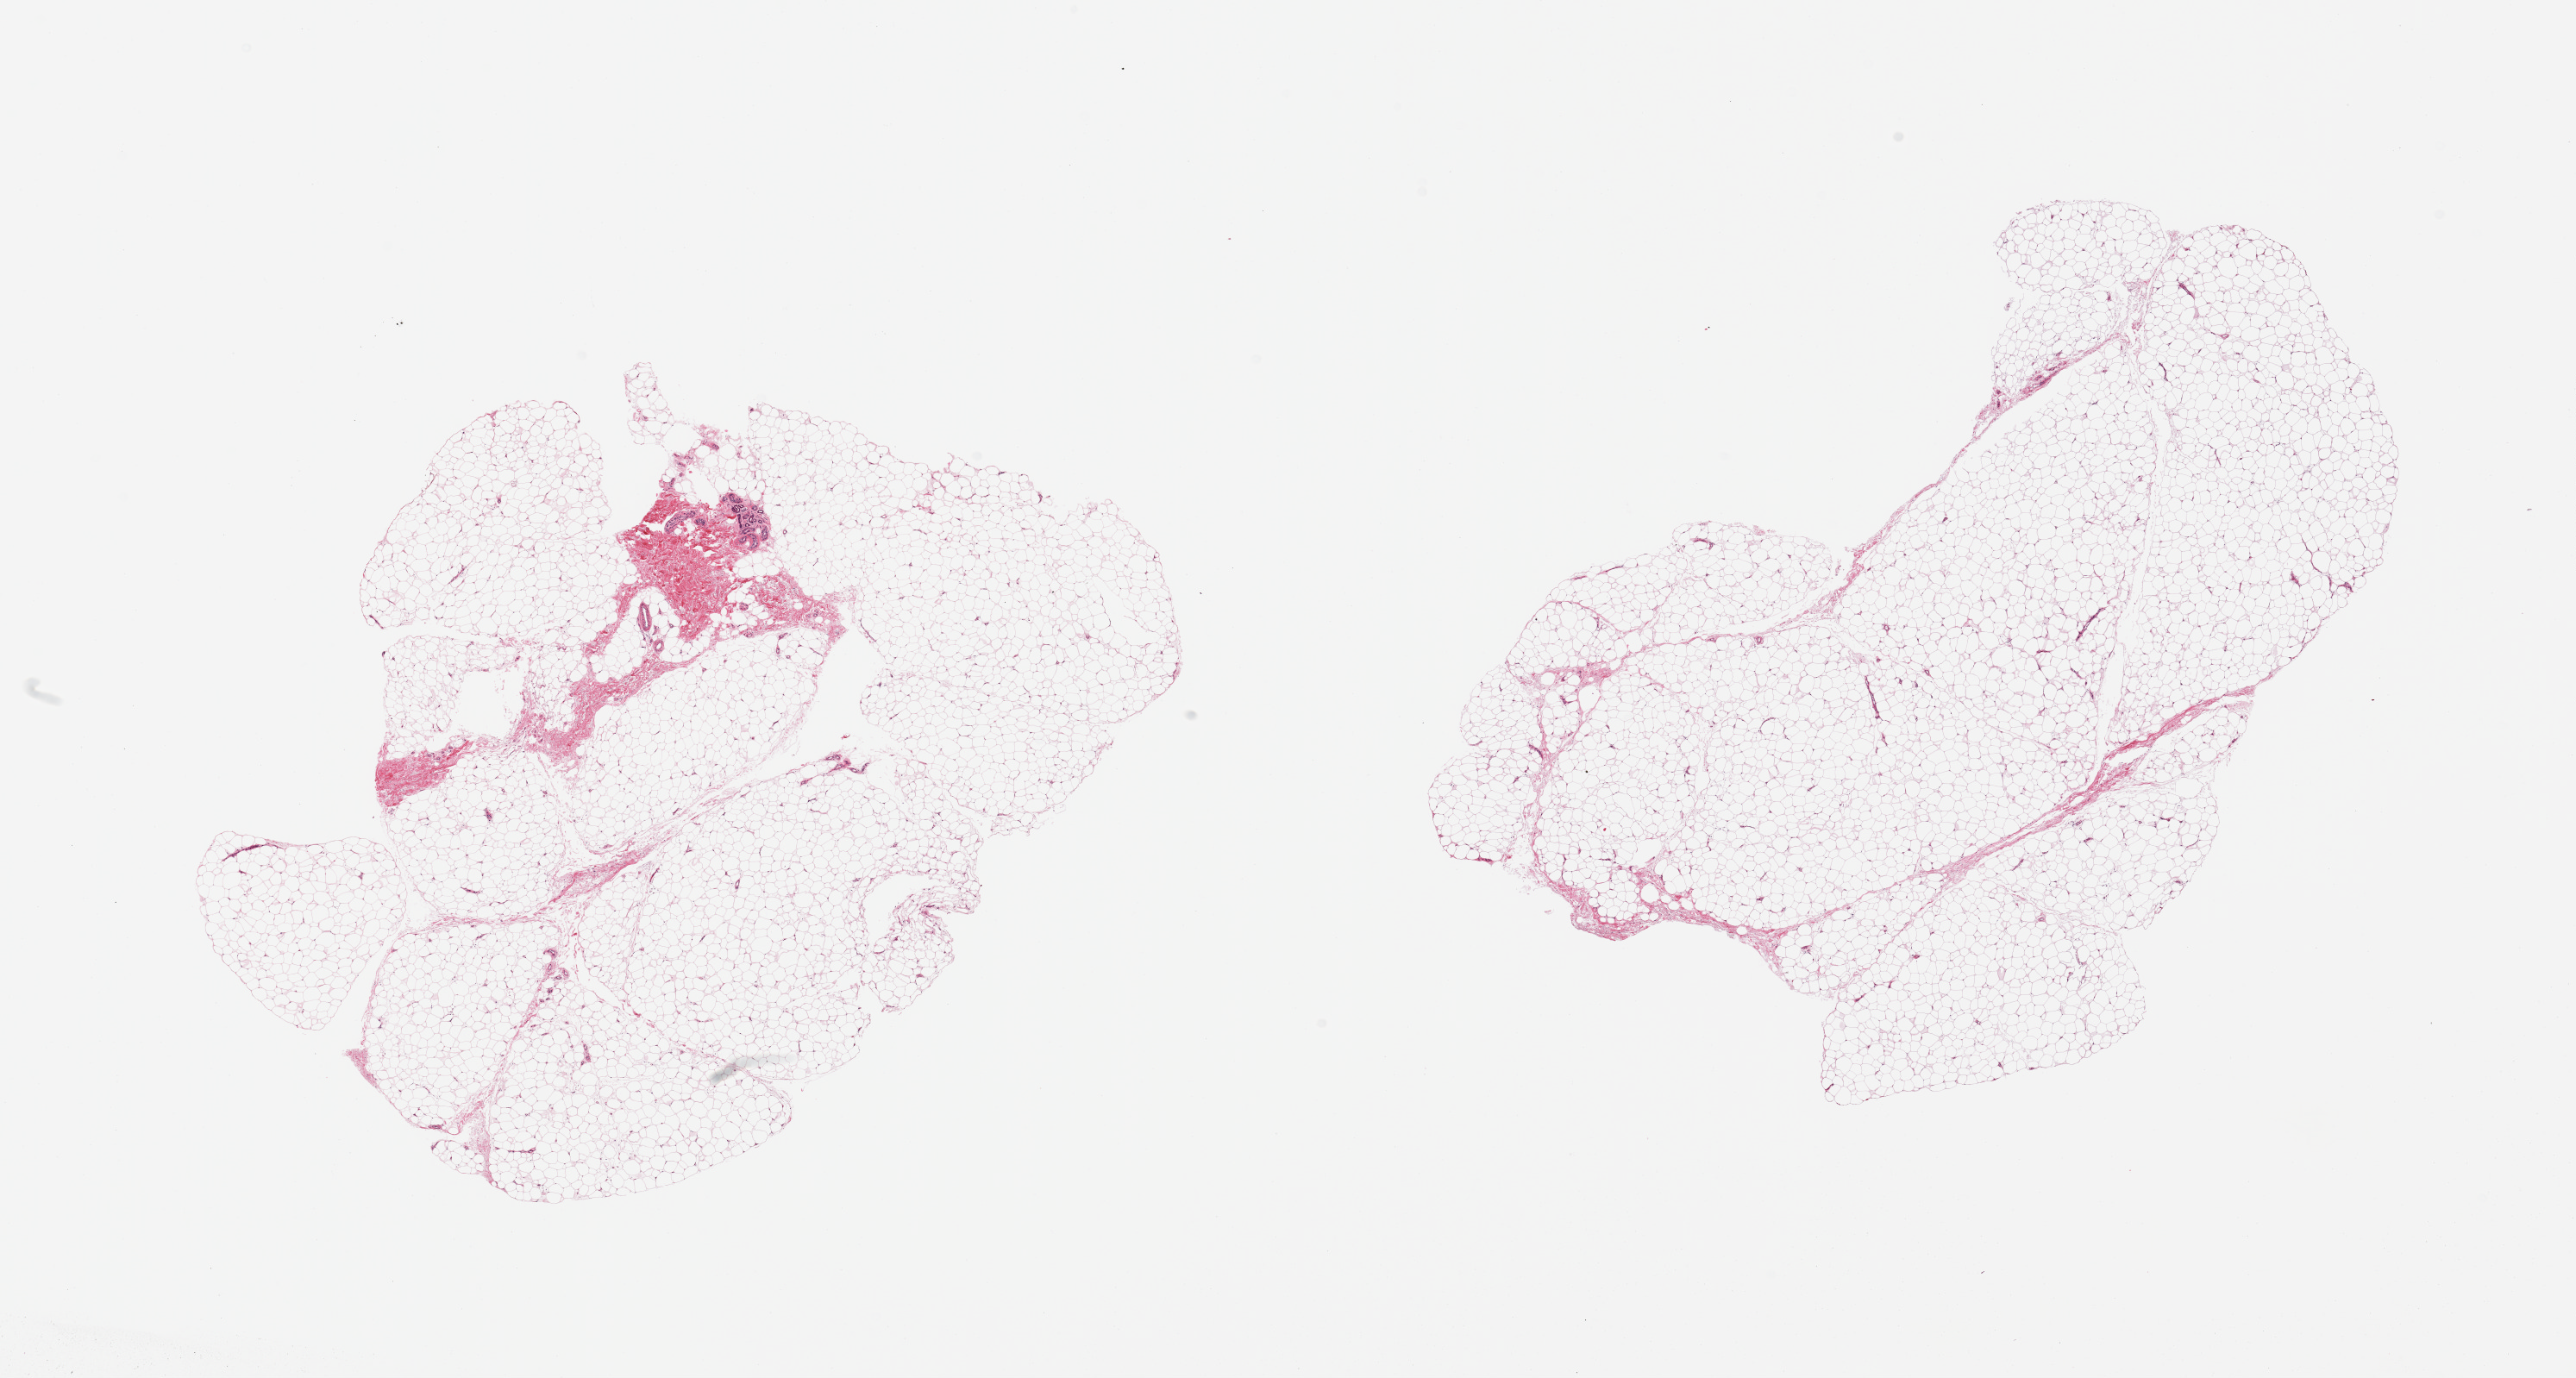
Whole-slide image, haematoxylin and eosin stain, low-resolution overview of the scanned area, about 23.6 x 12.6 mm. PAXgene-fixed paraffin-embedded (PFPE) section. Target tissue: adipose tissue. Donor tissue sample. Donor: male.
Review note (as recorded): 2 pieces; 0.6 sq mm sweat gland and dermal collagen complex.